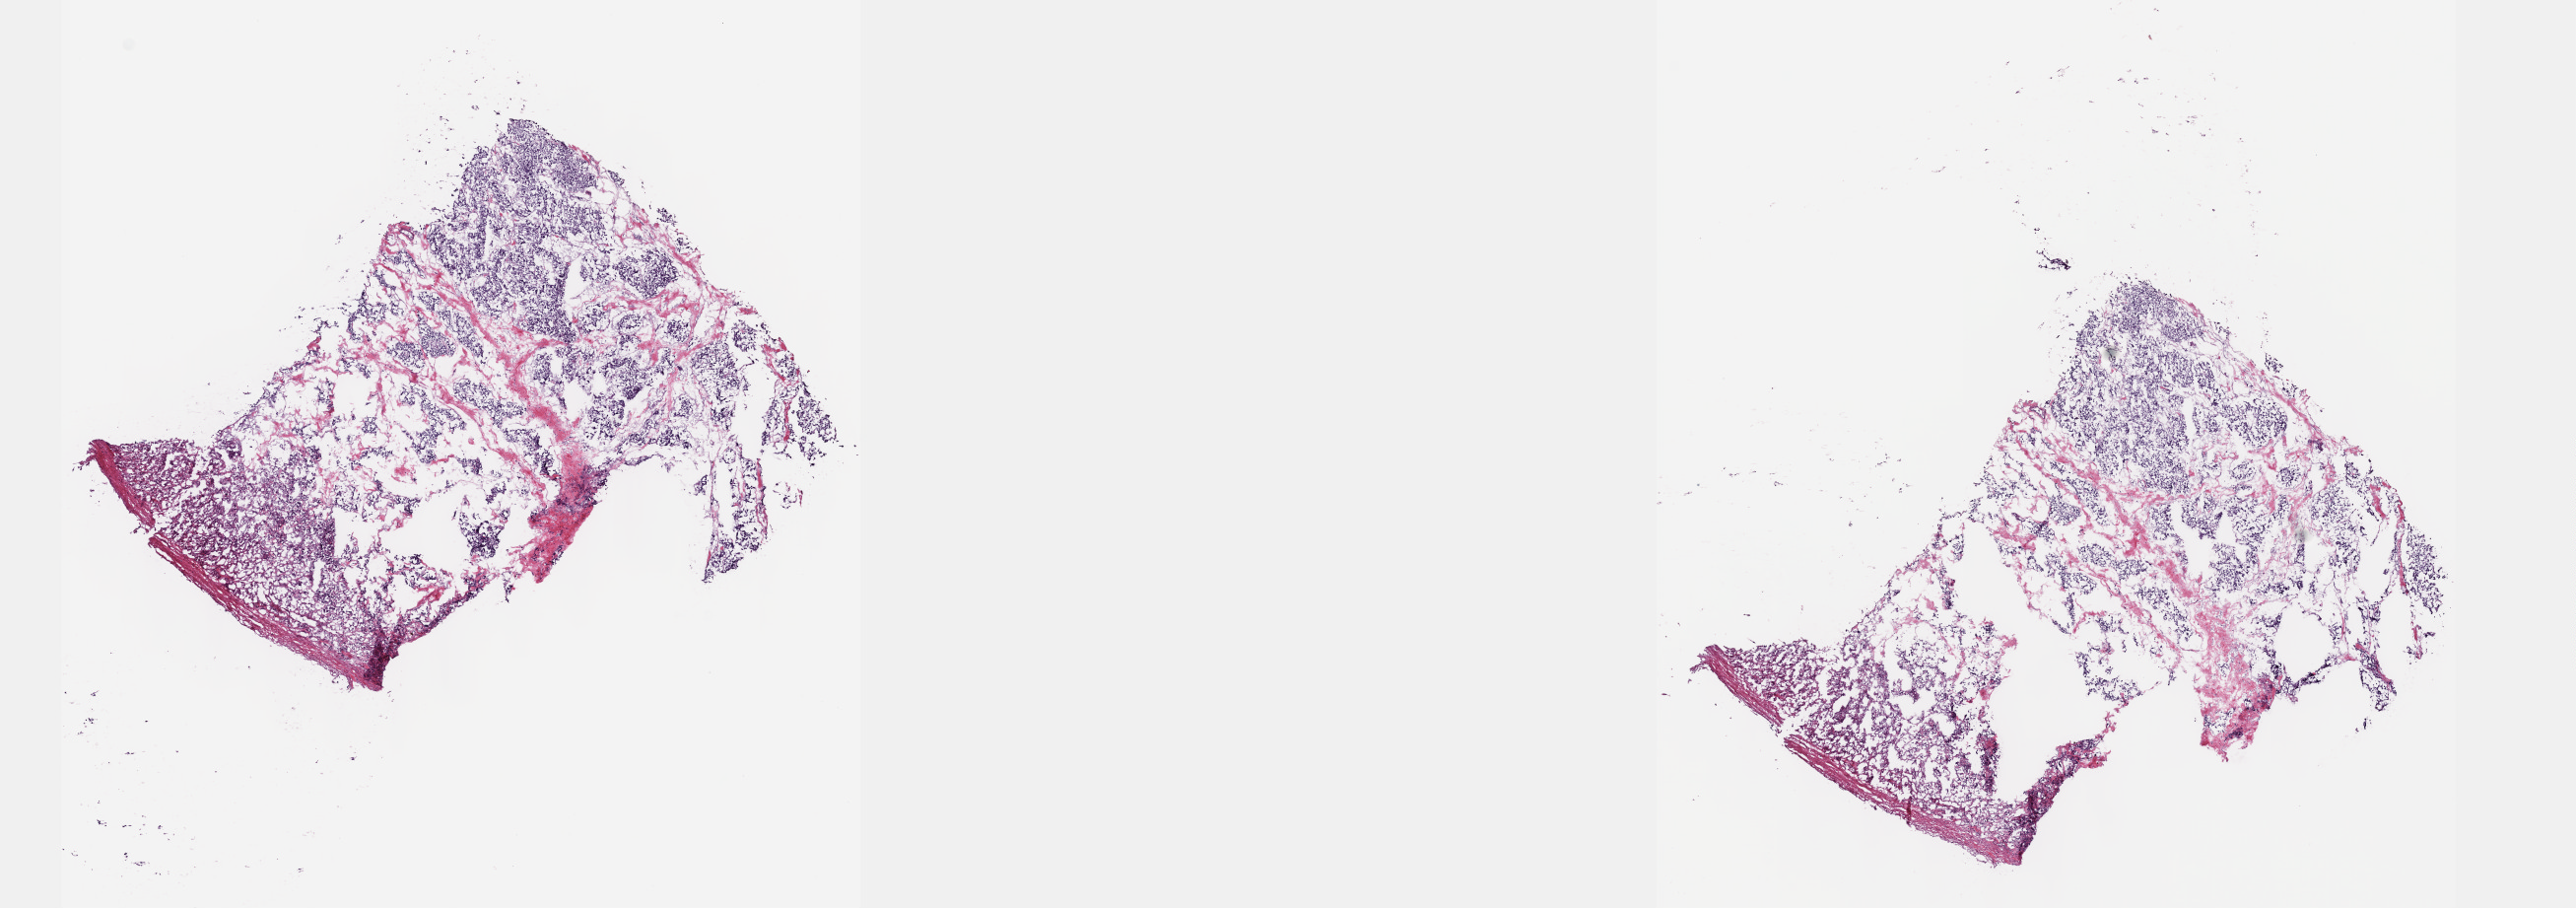
Digitized H&E tissue section (whole slide), whole scanned area (about 21.1 x 7.4 mm) shown as a low-resolution overview. Frozen section from the top of the tissue portion. Adrenal gland, primary tumour sample. Male patient; age at initial diagnosis 76 years. Composition of this section per pathologist review: tumour cells 95%, tumour nuclei 99%, normal cells 0%, stromal cells 5%, necrosis 0%. Inflammatory infiltration, as recorded: lymphocyte infiltration 0%, monocyte infiltration 0%, neutrophil infiltration 0%.
- histologic diagnosis: Pheochromocytoma, malignant